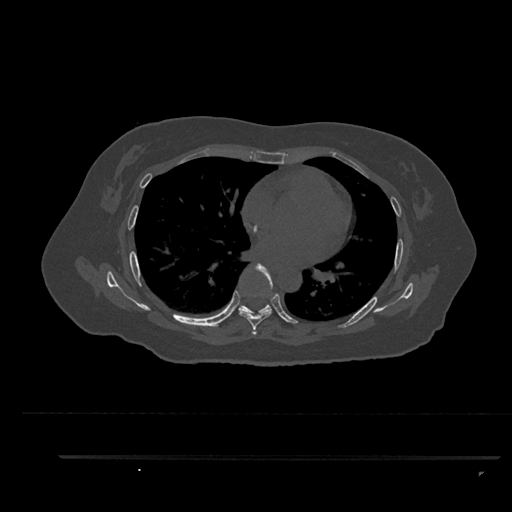
CT including the spine, one axial slice. Position 537 of 797 along the scan axis. Bone window (W 1800 / L 400 HU). 512 × 512 image matrix, field of view 408 × 408 mm. Patient: female, 44 years. From the clinical record (not read from this slice): primary cancer: renal.
Annotated regions visible in this slice (semi-automatic segmentation, software-assisted and operator-edited):
- T6 vertebra: bounding box [x1, y1, x2, y2] px = [239, 263, 273, 335]
- T7 vertebra: [238, 304, 272, 315]